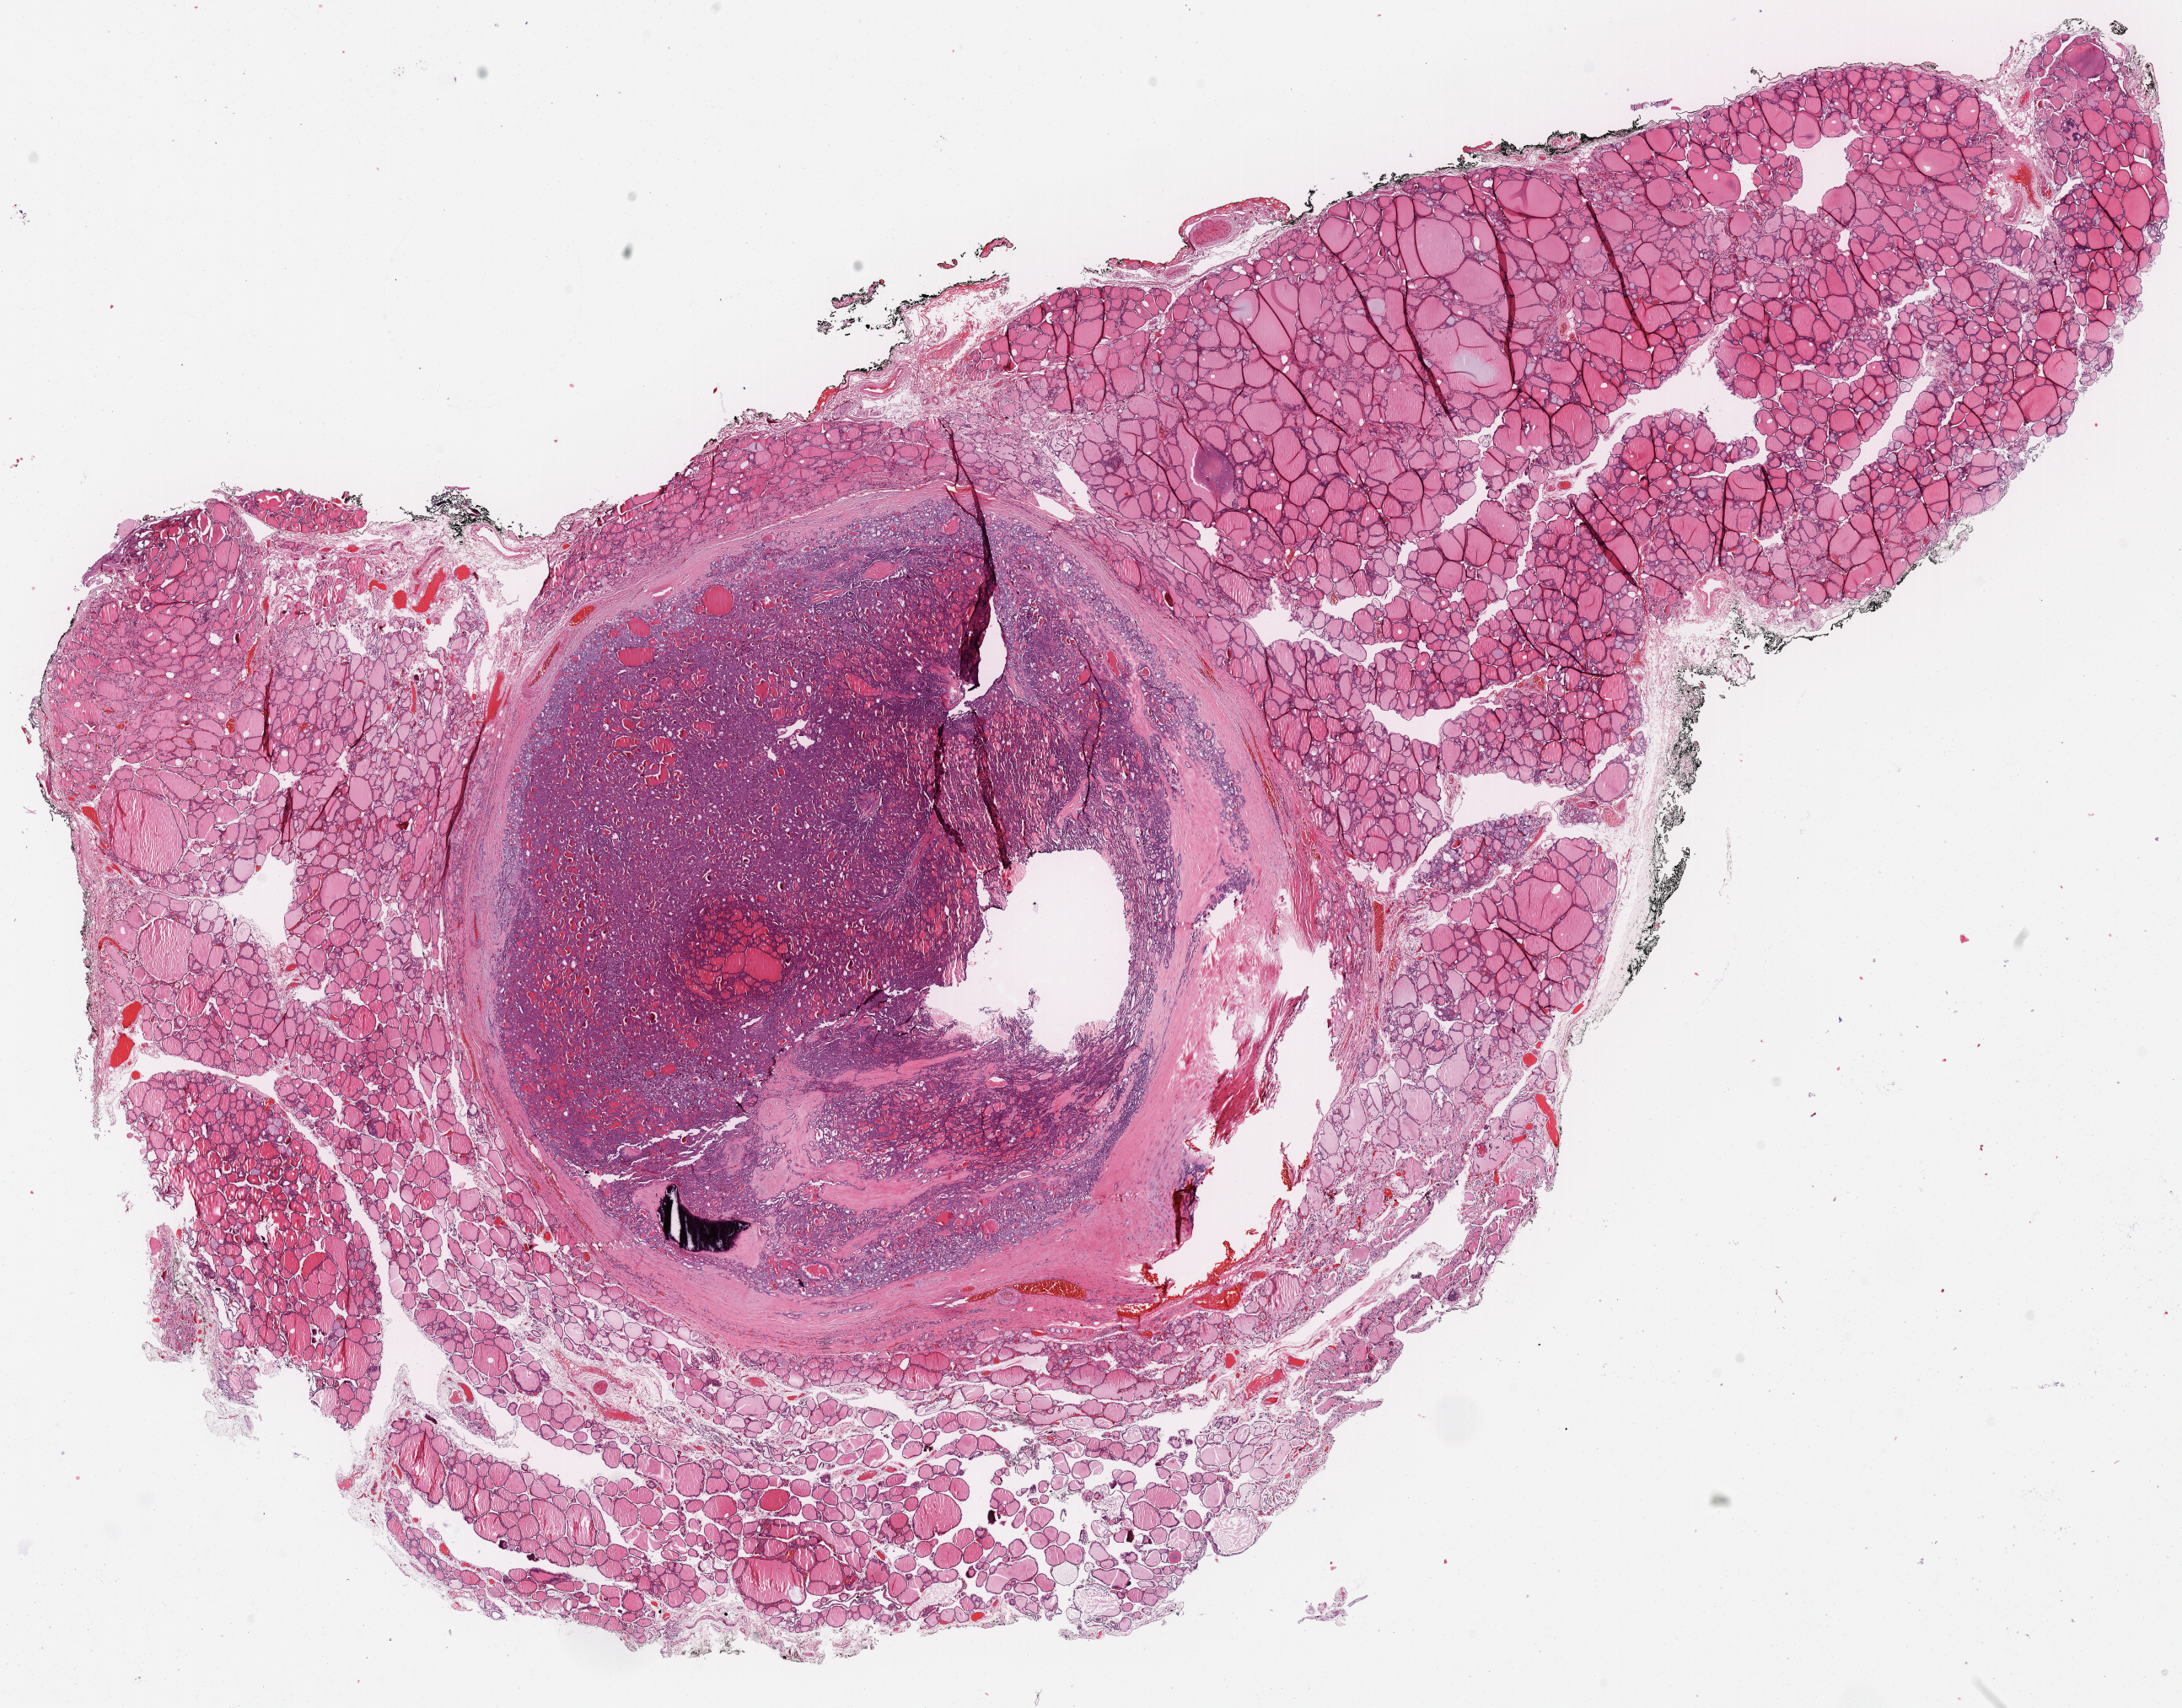
Whole-slide histology image, Hematoxylin and eosin (H&E) stained, a low-resolution overview of the entire scanned area, about 20.4 x 16.0 mm (slide scanned at 40x); FFPE section; primary tumour sample from the thyroid. Patient: male, age at initial diagnosis 29 years.
* AJCC pathologic stage: I
* diagnosis: Papillary adenocarcinoma, NOS (thyroid gland)